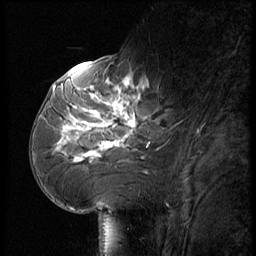
Breast MRI (dynamic contrast-enhanced), one sagittal slice; position 26 of 56 along the scan axis; dynamic contrast-enhanced series, image 2 of 3 at this slice position (ordered by acquisition); 1.5 T; TE 4.2 ms, TR 9 ms; 256 × 256 image matrix, field of view 180 × 180 mm. Female patient, age 61 years. Case-level facts recorded for this patient, not image findings: setting: breast cancer imaged before/during neoadjuvant chemotherapy; receptor status: HR-positive, HER2-negative.
Annotated regions visible in this slice (semi-automatic segmentation, software-assisted and operator-edited):
- analysis volume of interest (the breast-tissue region the enhancement analysis was run in; not a lesion): bounding box <65,74,184,175> (left, top, right, bottom; pixels)
- tumour enhancement mask (voxels above the 140 % enhancement threshold inside the analysis volume of interest): <65,81,150,163>